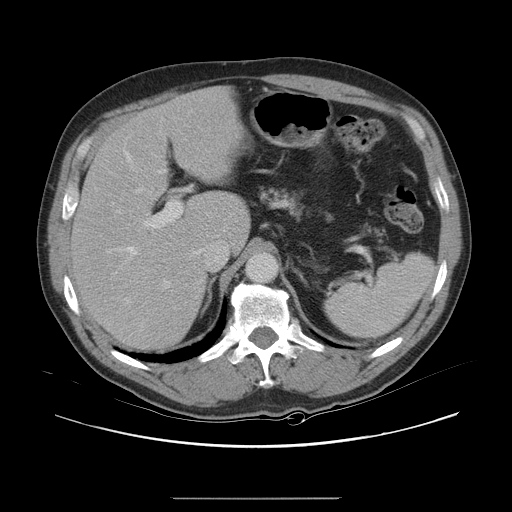
Contrast-enhanced abdominal CT, one axial slice. Slice 17 of 40 in the series (ordered by position). 120 kVp. Intravenous contrast given. Soft-tissue window (W 400 / L 40 HU). 5 mm slice thickness. 512 × 512 image matrix. Male patient, age 64 years. From the clinical record (not read from this slice): diagnosis: colorectal cancer liver metastases, imaged before liver resection; multiple liver metastases: yes; largest metastasis: 3.2 cm.
Outlined on this slice (manually delineated by an expert):
- hepatic veins: bounding box [x1, y1, x2, y2] px = [126, 187, 221, 303]
- liver: [74, 90, 250, 348]
- planned liver remnant (the part of the liver to remain after resection): [89, 90, 250, 247]
- portal vein (with intrahepatic branches): [125, 152, 182, 287]